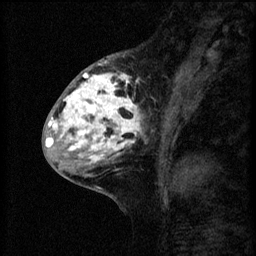
Breast MRI (dynamic contrast-enhanced), one sagittal slice; position 26 of 60 along the scan axis; 3 images stored at this slice position (order not interpretable as contrast timing); 1.5 T; TE 4.2 ms, TR 8.2 ms; 2 mm slice thickness; 256 × 256 image matrix. Female patient, age 41 years.
Annotated regions visible in this slice (semi-automatic segmentation, software-assisted and operator-edited):
- analysis volume of interest (the breast-tissue region the enhancement analysis was run in; not a lesion): box from (x=53, y=62) to (x=158, y=175) px
- tumour enhancement mask (voxels above the 70 % enhancement threshold inside the analysis volume of interest): (x=53, y=62)–(x=143, y=163)